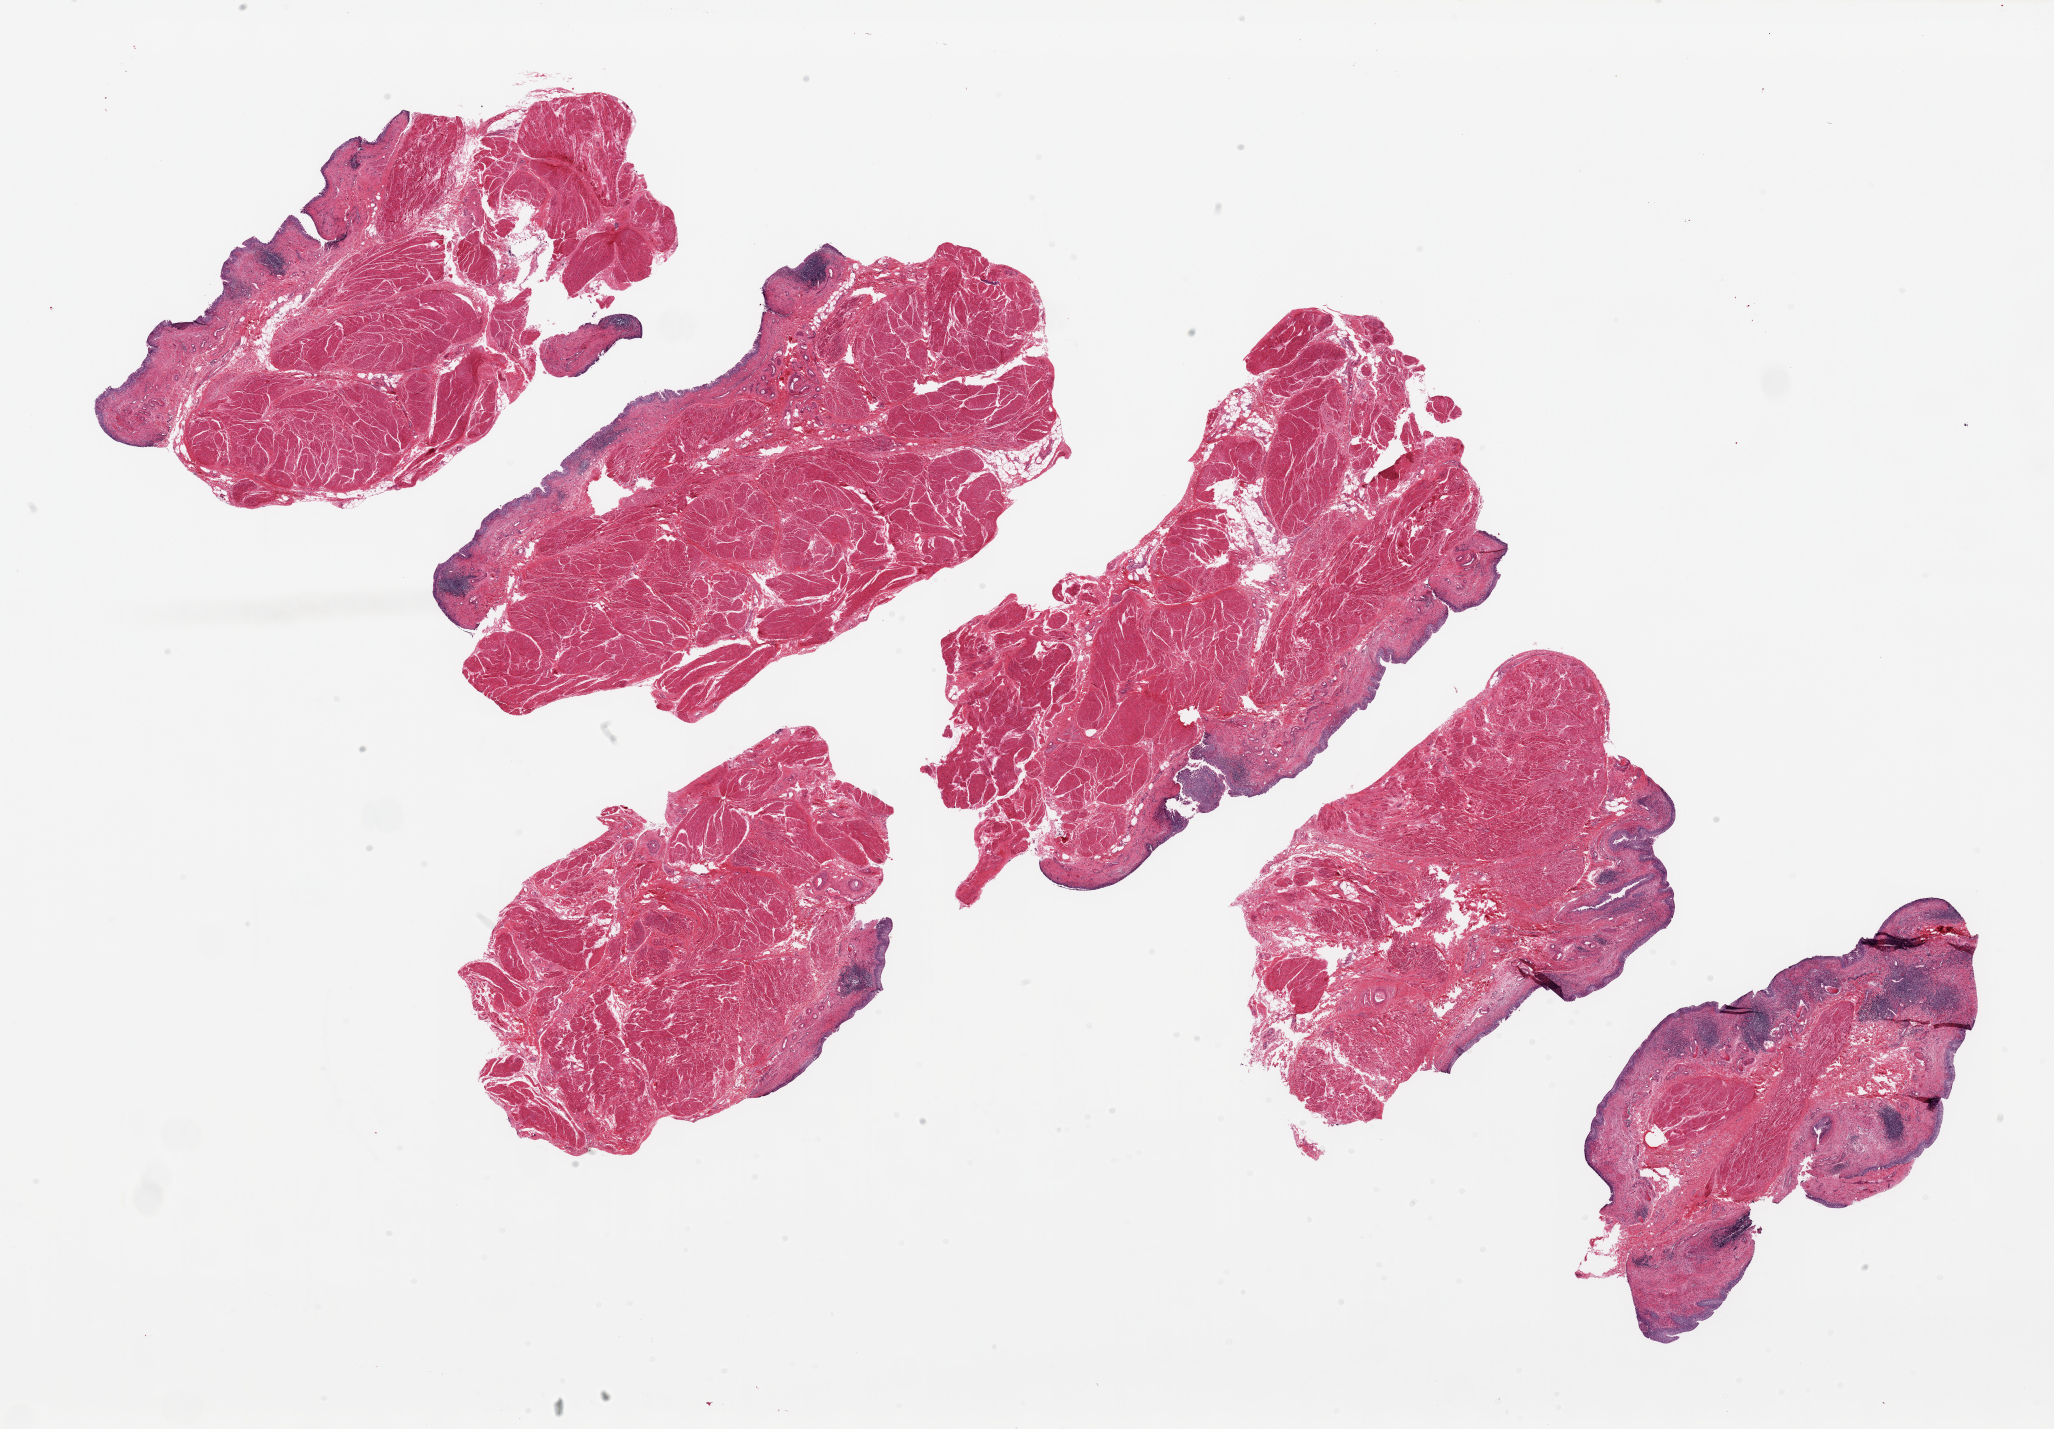
Digitized haematoxylin and eosin-stained section — a low-resolution overview of the entire scanned area, about 32.5 x 22.6 mm (acquisition: 20x scan); PAXgene-fixed paraffin-embedded (PFPE) section; sampled site (target tissue): urinary bladder; tissue donor sample. Female donor.
- reviewer comment on this tissue sample: 6 ~6-10x4mm pieces. Urothelium unusually well- preserved, with patchy chronic cystitis. ~ 1% of specimen thickness